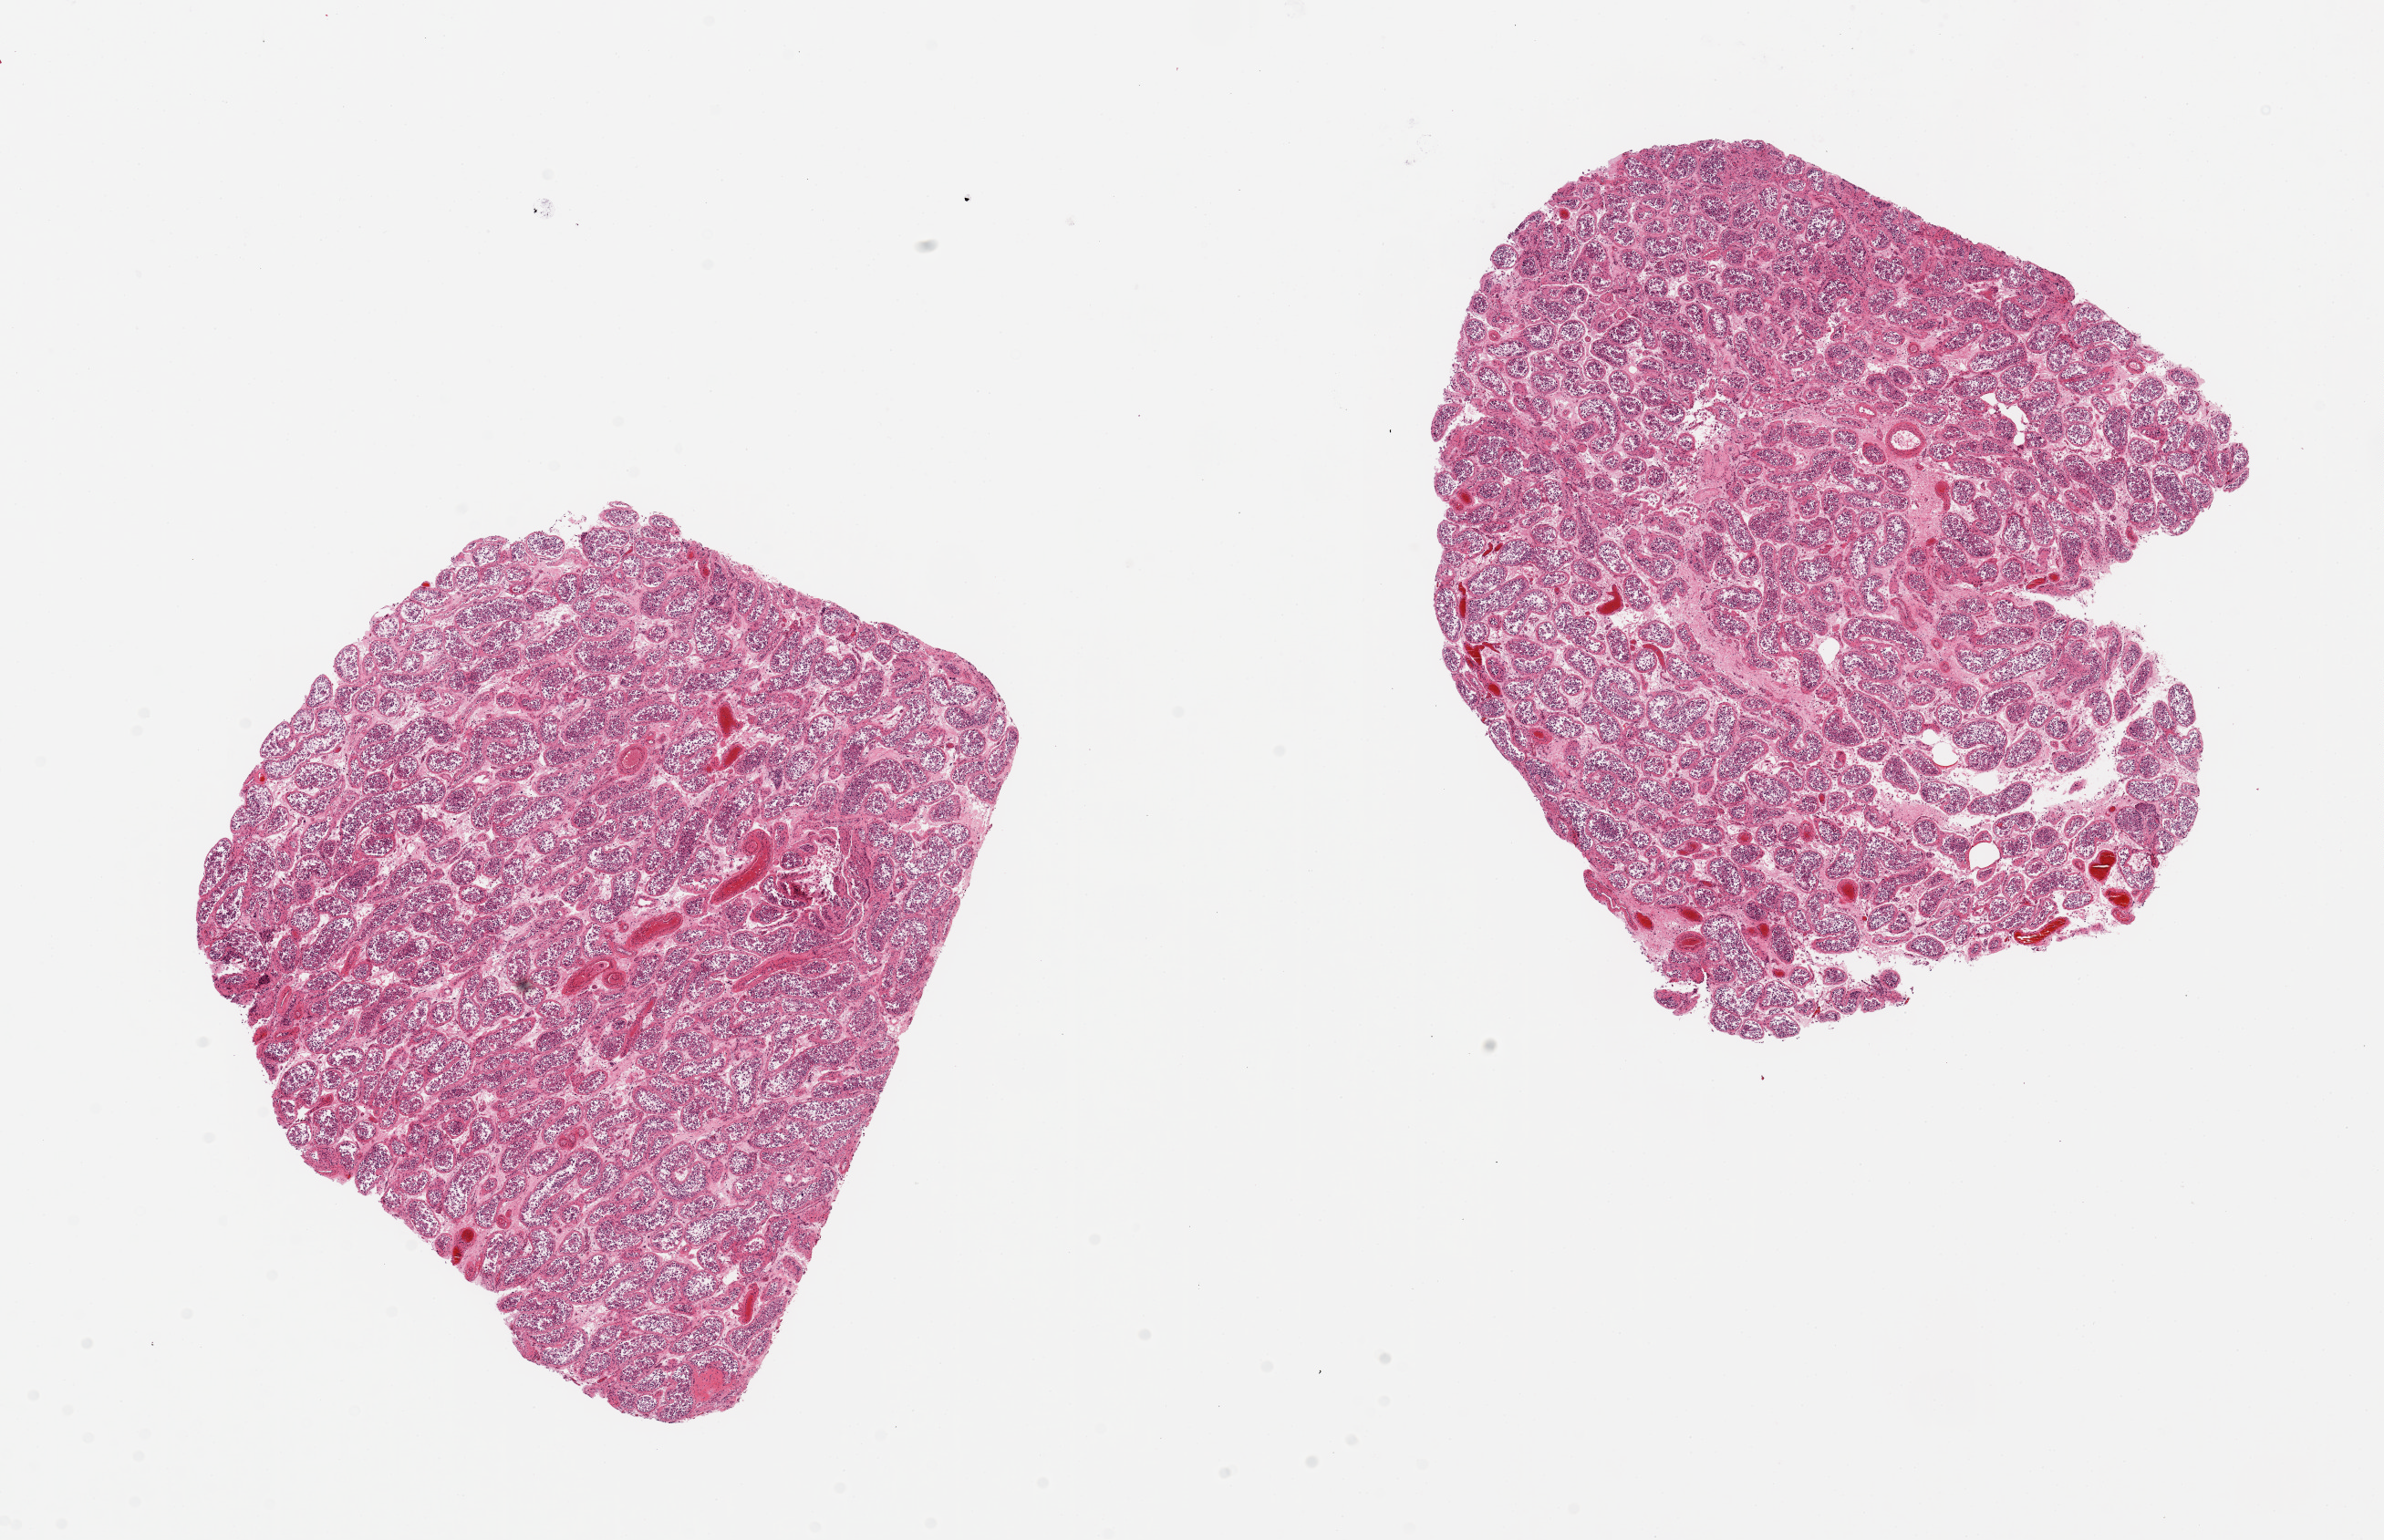
Whole-slide image, haematoxylin and eosin stain, brightfield — shown as a low-resolution overview of the whole scanned area (about 20.7 x 13.4 mm); PAXgene-fixed, paraffin-embedded tissue; section of testis (target tissue); tissue donor sample.
• pathologist's review note for this sample: 2 pieces, 7x5 & 8x7mm; spermatogeneisis present, but badly autolyzed